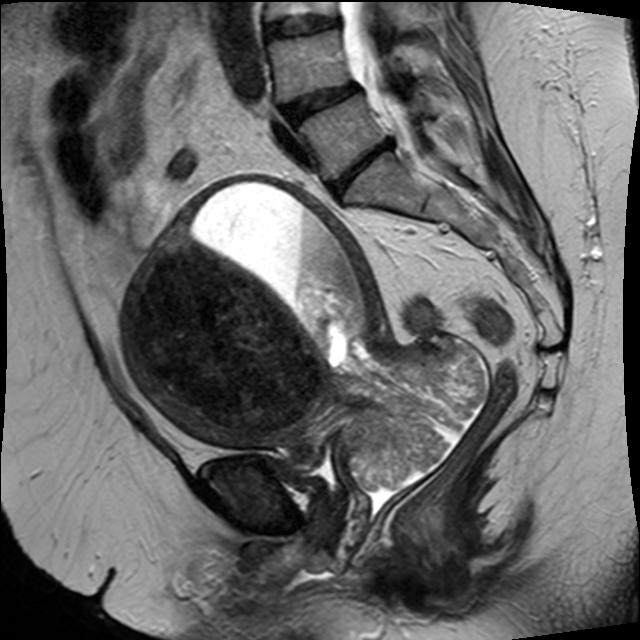
Pelvic MRI for cervical cancer, one sagittal slice. Slice 17 of 34 in the series (ordered by position). T2-weighted. 1.5 T. TE 89 ms, TR 3320 ms. 4 mm slice thickness. 640 × 640 image matrix, field of view 260 × 260 mm. Female patient, age 50 years.
Structures marked on this image (expert manual segmentation):
- uterus and cervix: bounding box (x1, y1, x2, y2) in pixels: (123, 172, 489, 493)